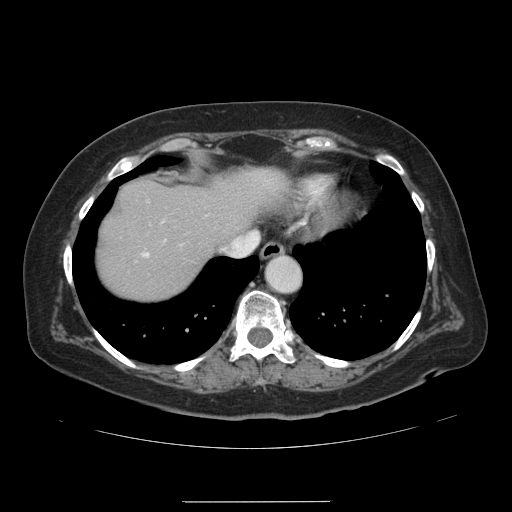
Contrast-enhanced abdominal CT, one axial slice; slice 118 of 141 in the series (ordered by position); intravenous contrast given; soft-tissue window (W 400 / L 40 HU); 2.5 mm slice thickness; 512 × 512 image matrix, field of view 393 × 393 mm. Female patient, age 74 years. From the clinical record (not read from this slice): diagnosis: colorectal cancer liver metastases, imaged before liver resection; multiple liver metastases: yes; largest metastasis: 7 cm; disease in both lobes: yes.
Annotated regions visible in this slice (expert manual segmentation):
- hepatic veins: bounding box [x1, y1, x2, y2] px = [221, 237, 241, 253]
- liver: [99, 170, 281, 298]
- planned liver remnant (the part of the liver to remain after resection): [99, 170, 281, 293]